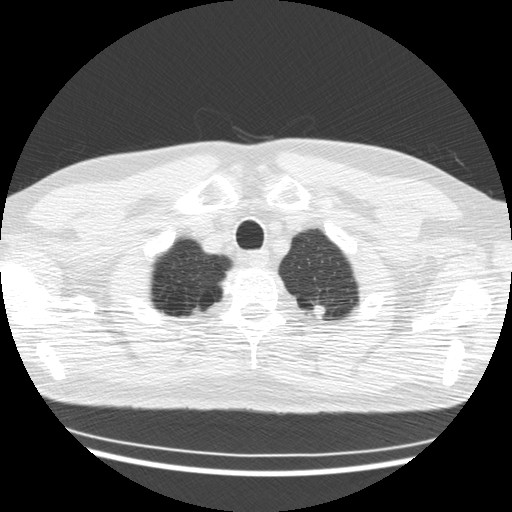
Low-dose screening chest CT, one axial slice. Position 158 of 176 along the scan axis. Reconstruction kernel STANDARD. 120 kVp. Lung window (W 1500 / L -600 HU). 2.5 mm slice thickness. 512 × 512 image matrix, field of view 360 × 360 mm.
Annotated regions visible in this slice (expert manual segmentation):
- lesion 1 (tumor, upper lobe of left lung): box from (x=314, y=305) to (x=326, y=318) px